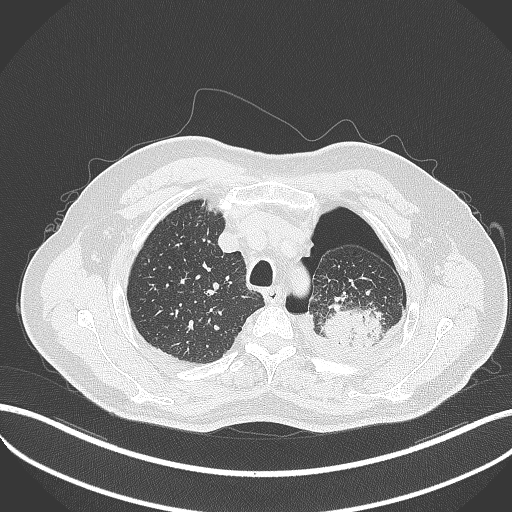
Chest CT, one axial slice; slice 410 of 464 in the series (ordered by position); lung window (W 1500 / L -600 HU); 512 × 512 image matrix. Patient: male, 76 years. From the clinical record (not read from this slice): clinical TNM (as recorded): T3 N0 M1b.
Structures marked on this image (bounding box drawn by a radiologist):
- lung tumour (recorded histology: adenocarcinoma): bounding box [x1, y1, x2, y2] px = [323, 304, 385, 347]